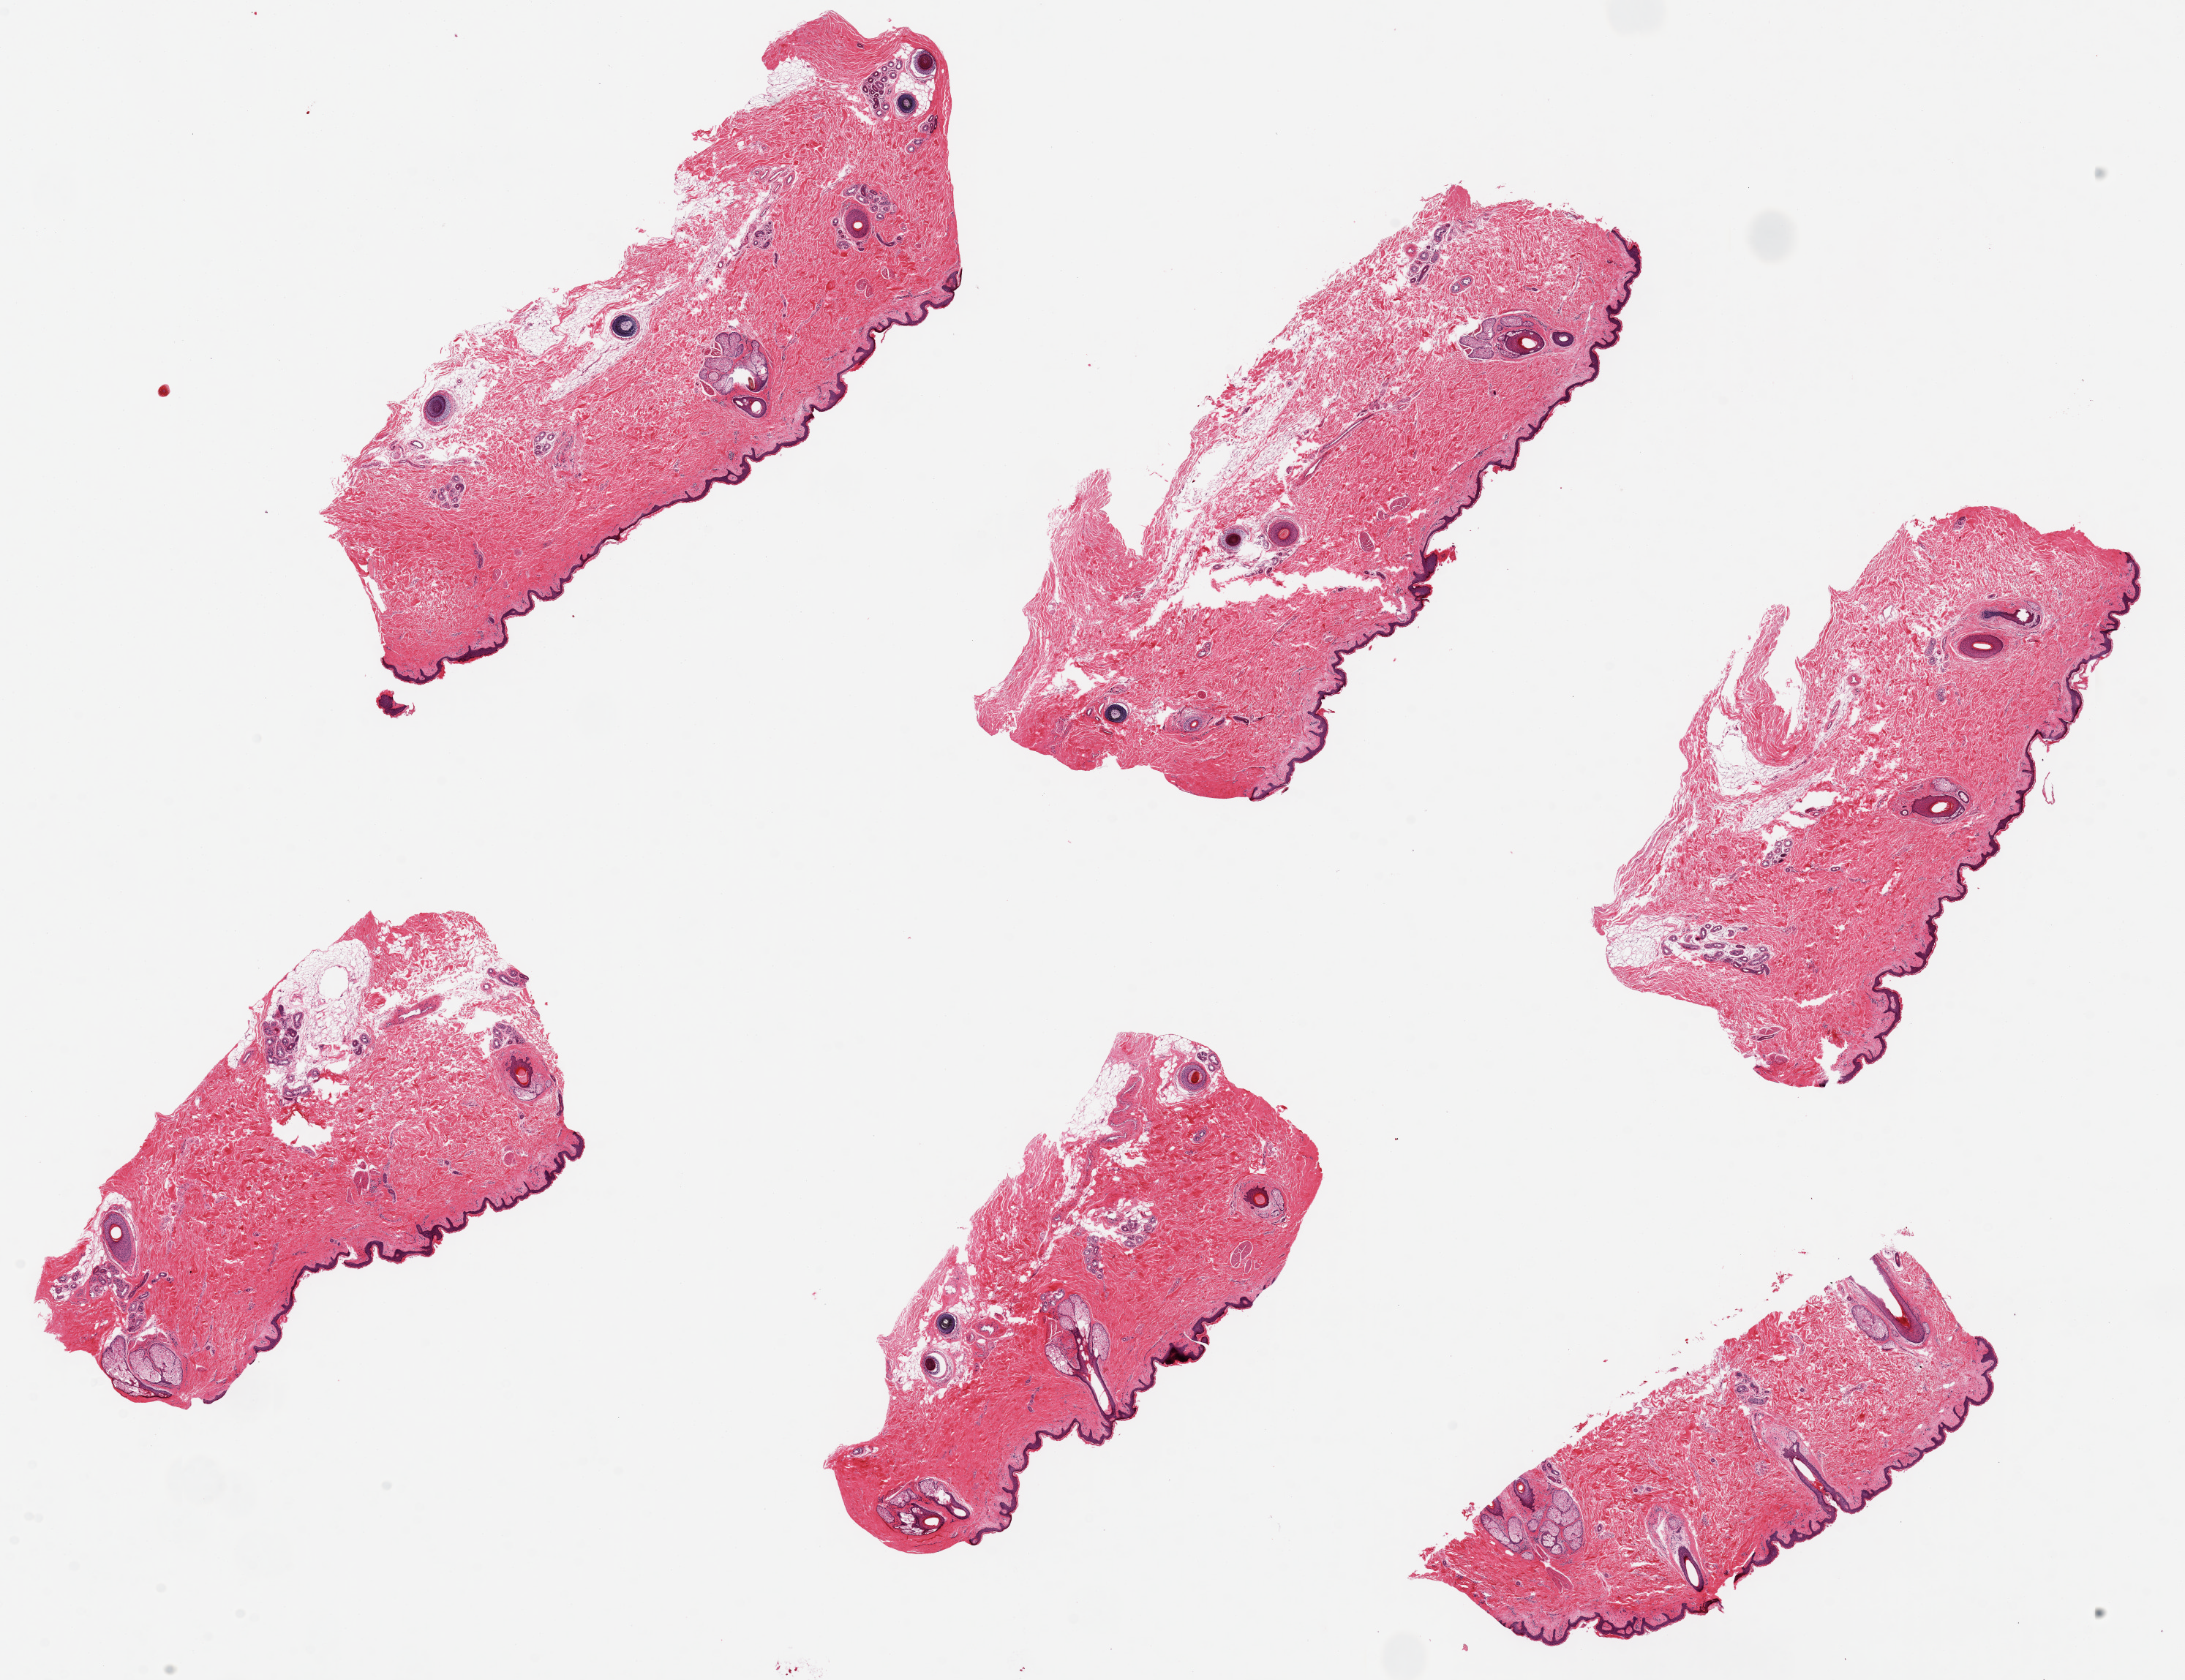
Hematoxylin and eosin (H&E) whole-slide image, whole scanned area (about 23.6 x 18.2 mm) shown as a low-resolution overview. PAXgene-fixed, paraffin-embedded tissue. Sampled site (target tissue): skin of suprapubic region. Tissue donor sample.
• reviewer comment on this tissue sample: 6 pieces, up to 9x3mm; subcutaneous fat is well trimmed